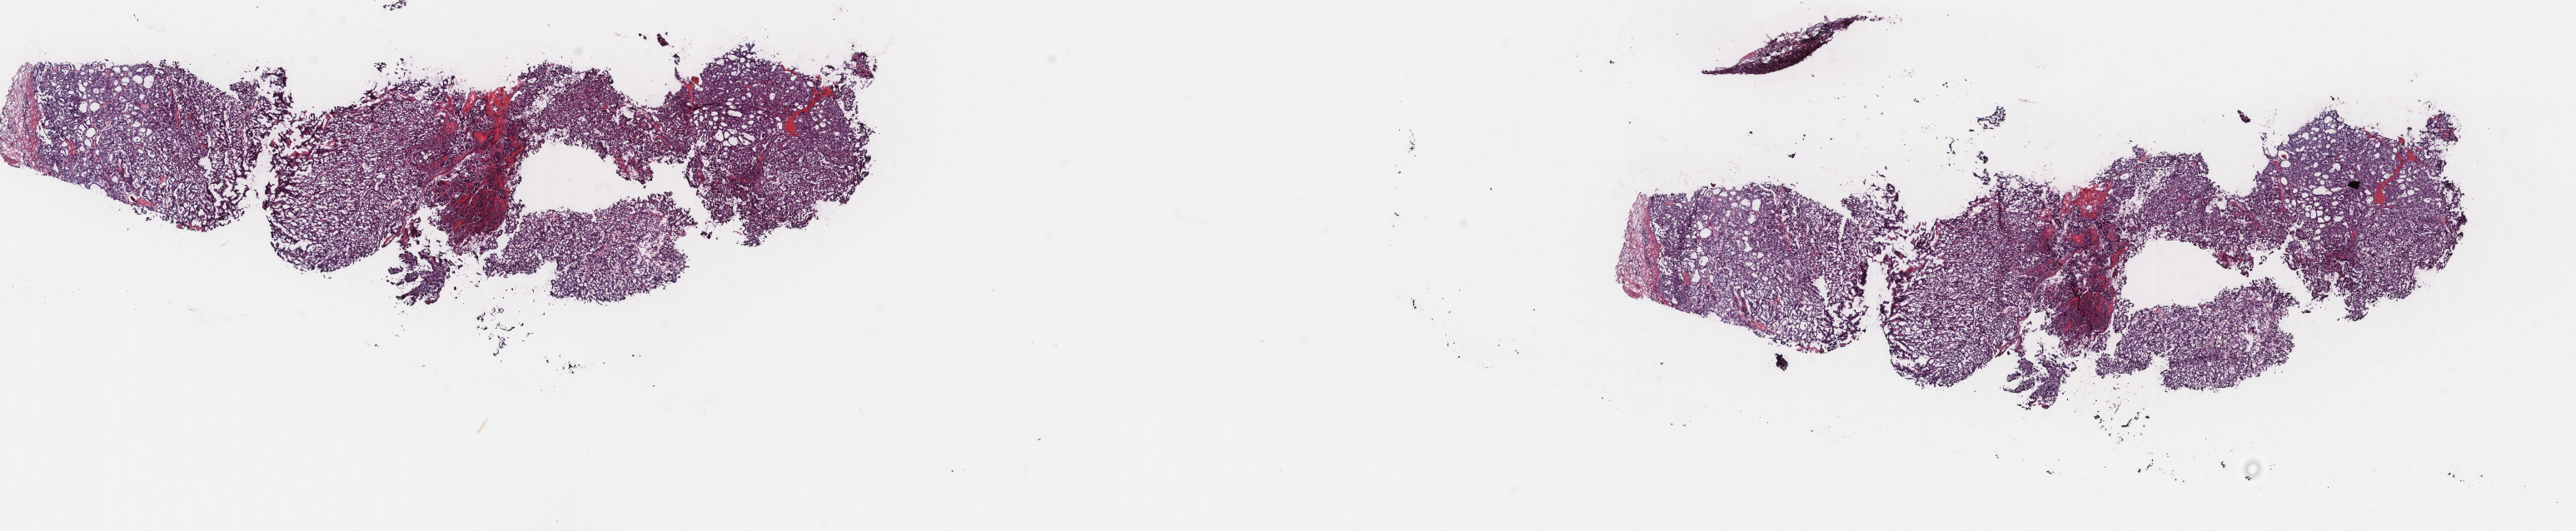
Hematoxylin and eosin (H&E) stained whole-slide image — shown as a low-resolution overview of the whole scanned area (about 24.6 x 5.1 mm). Frozen section. Sample: primary tumour, thyroid. Patient: male, age at initial diagnosis 62 years. Slide review estimates, as recorded: tumour cells 80%, tumour nuclei 90%, normal cells 0%, stromal cells 20%, necrosis 0%. Infiltration values recorded for this section: lymphocyte infiltration 5%, monocyte infiltration 0%, neutrophil infiltration 0%.
TNM: T2 N0 MX. Lymph nodes positive (case pathology): 0 of 12 examined. AJCC pathologic stage: II (7th edition). Diagnosis: Papillary adenocarcinoma, NOS (thyroid gland).